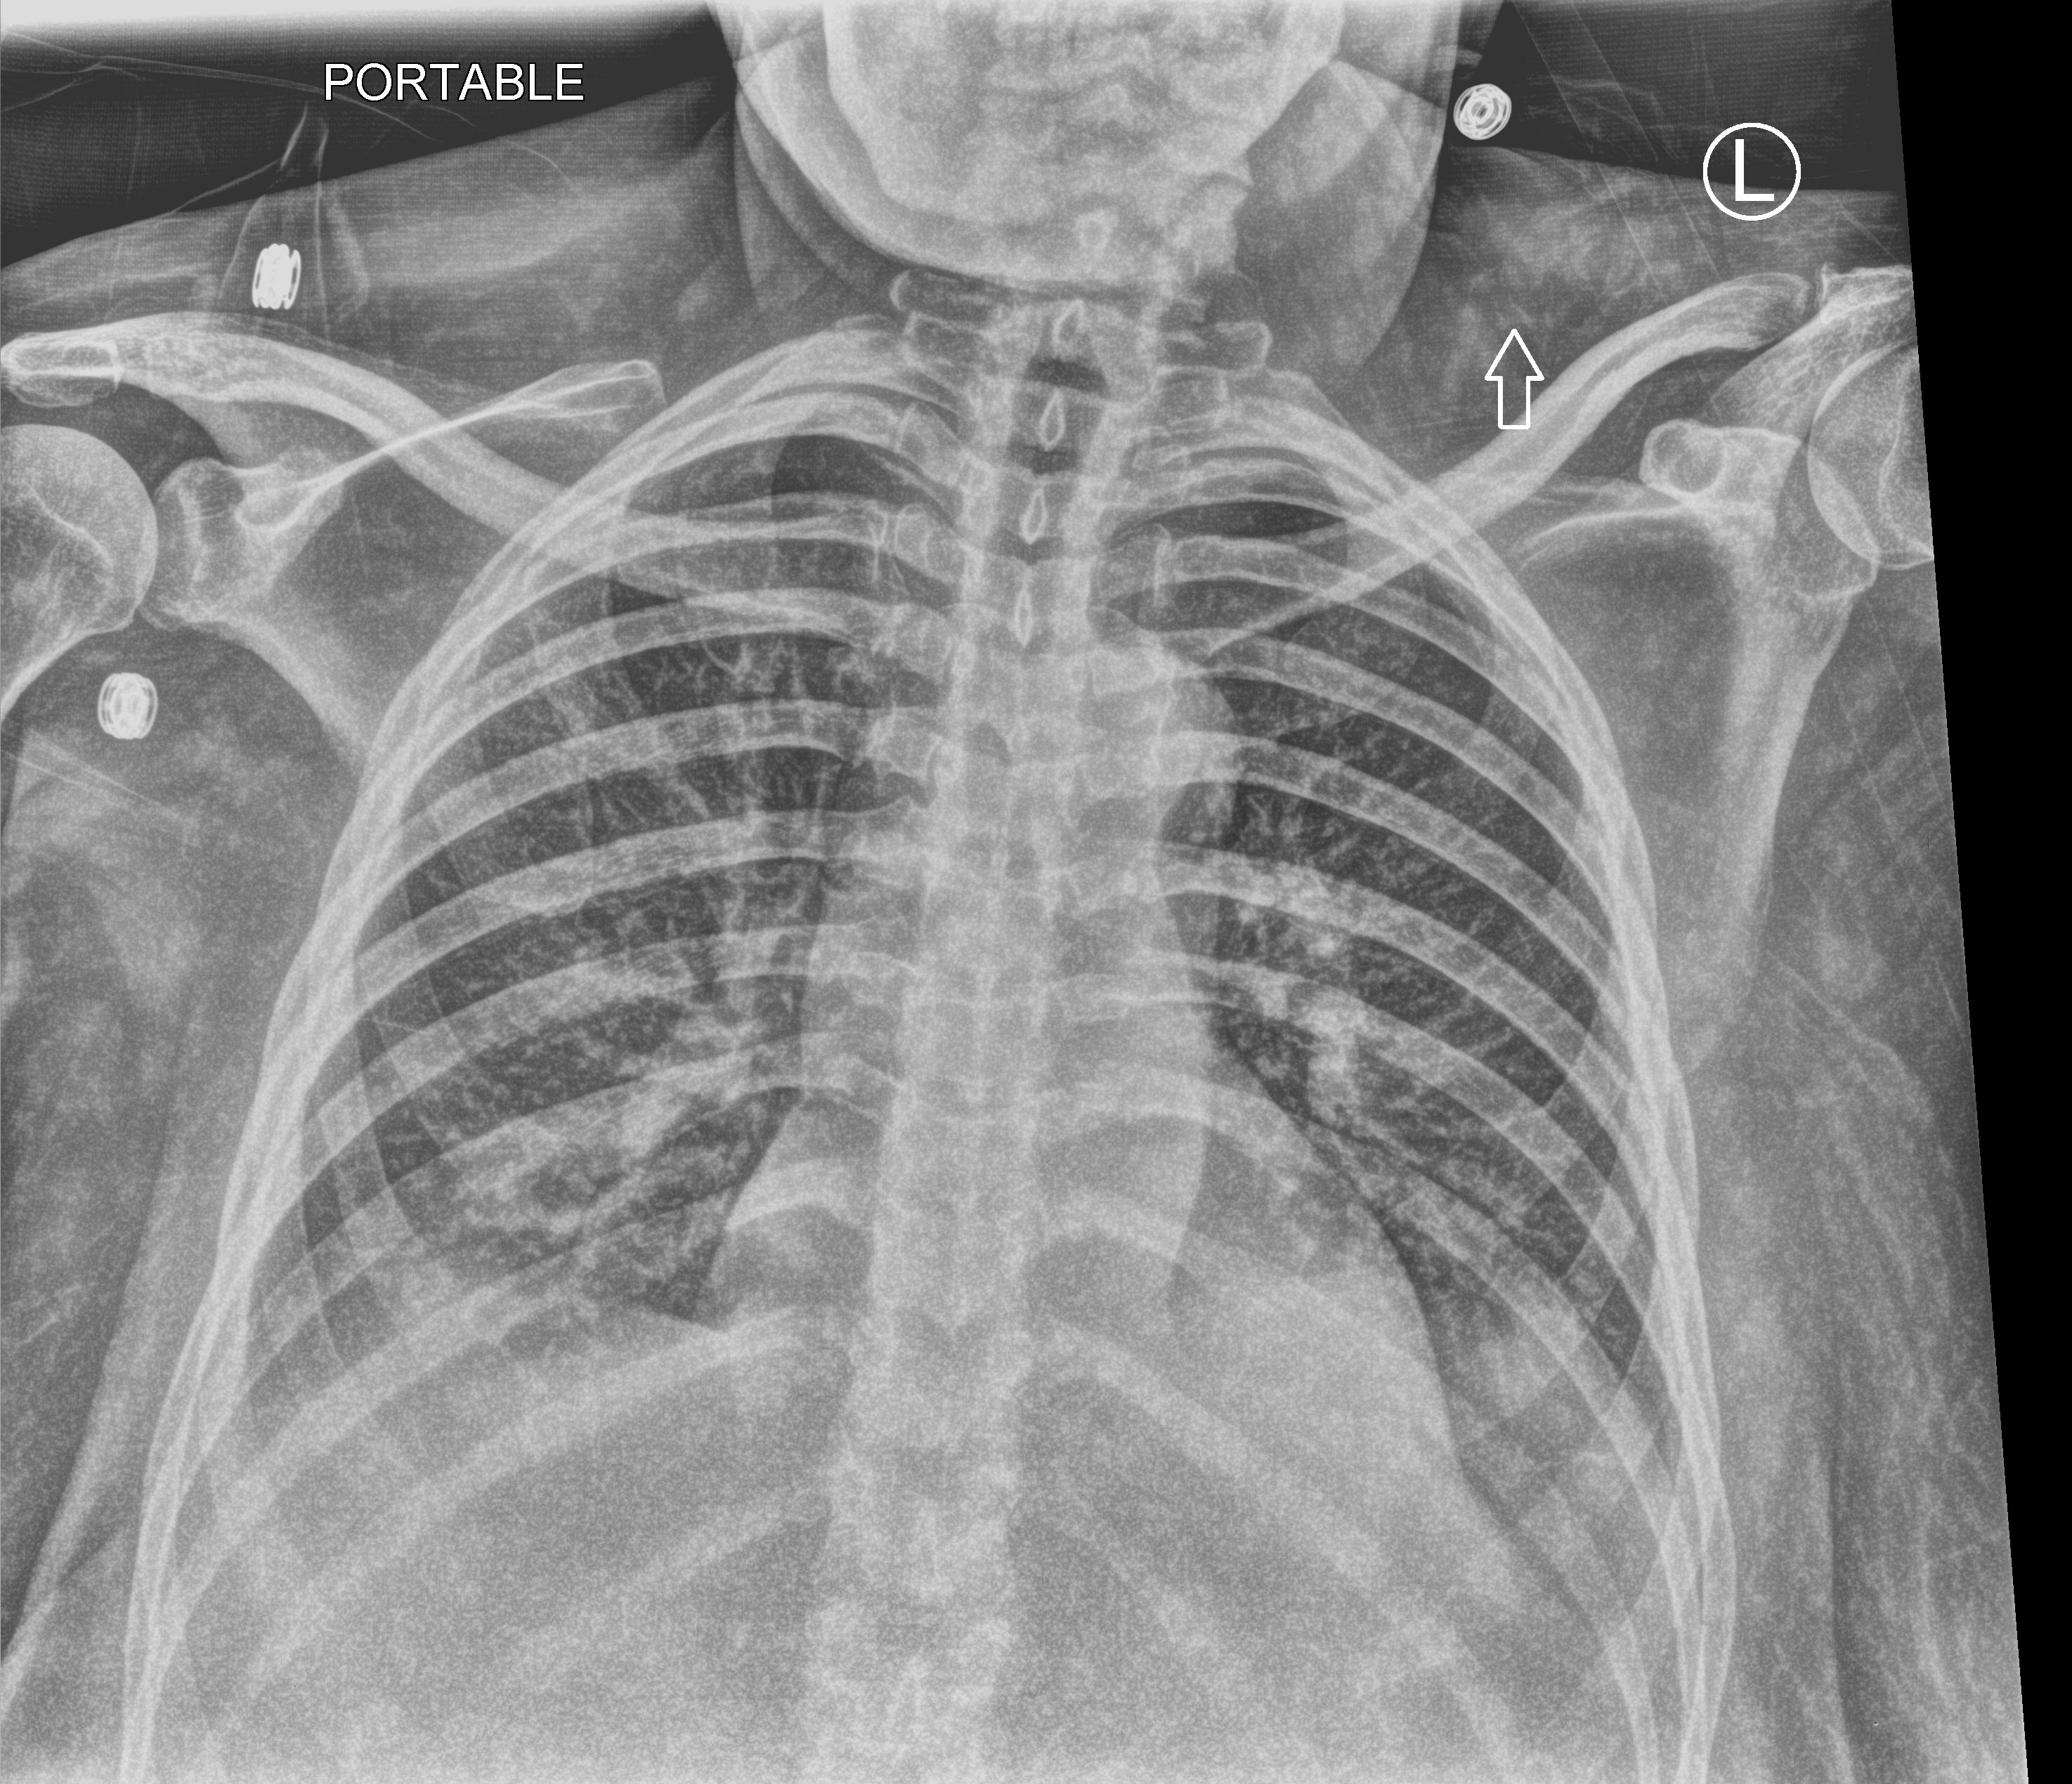
Chest X-ray (portable); anteroposterior (AP) projection. Female patient hospitalised with COVID-19, age 18–59 years.
Hospital-stay facts (about this admission, not read from this image; timing relative to this image not recorded): admitted to intensive care during this hospital stay: no; smoking status (admission record): former.